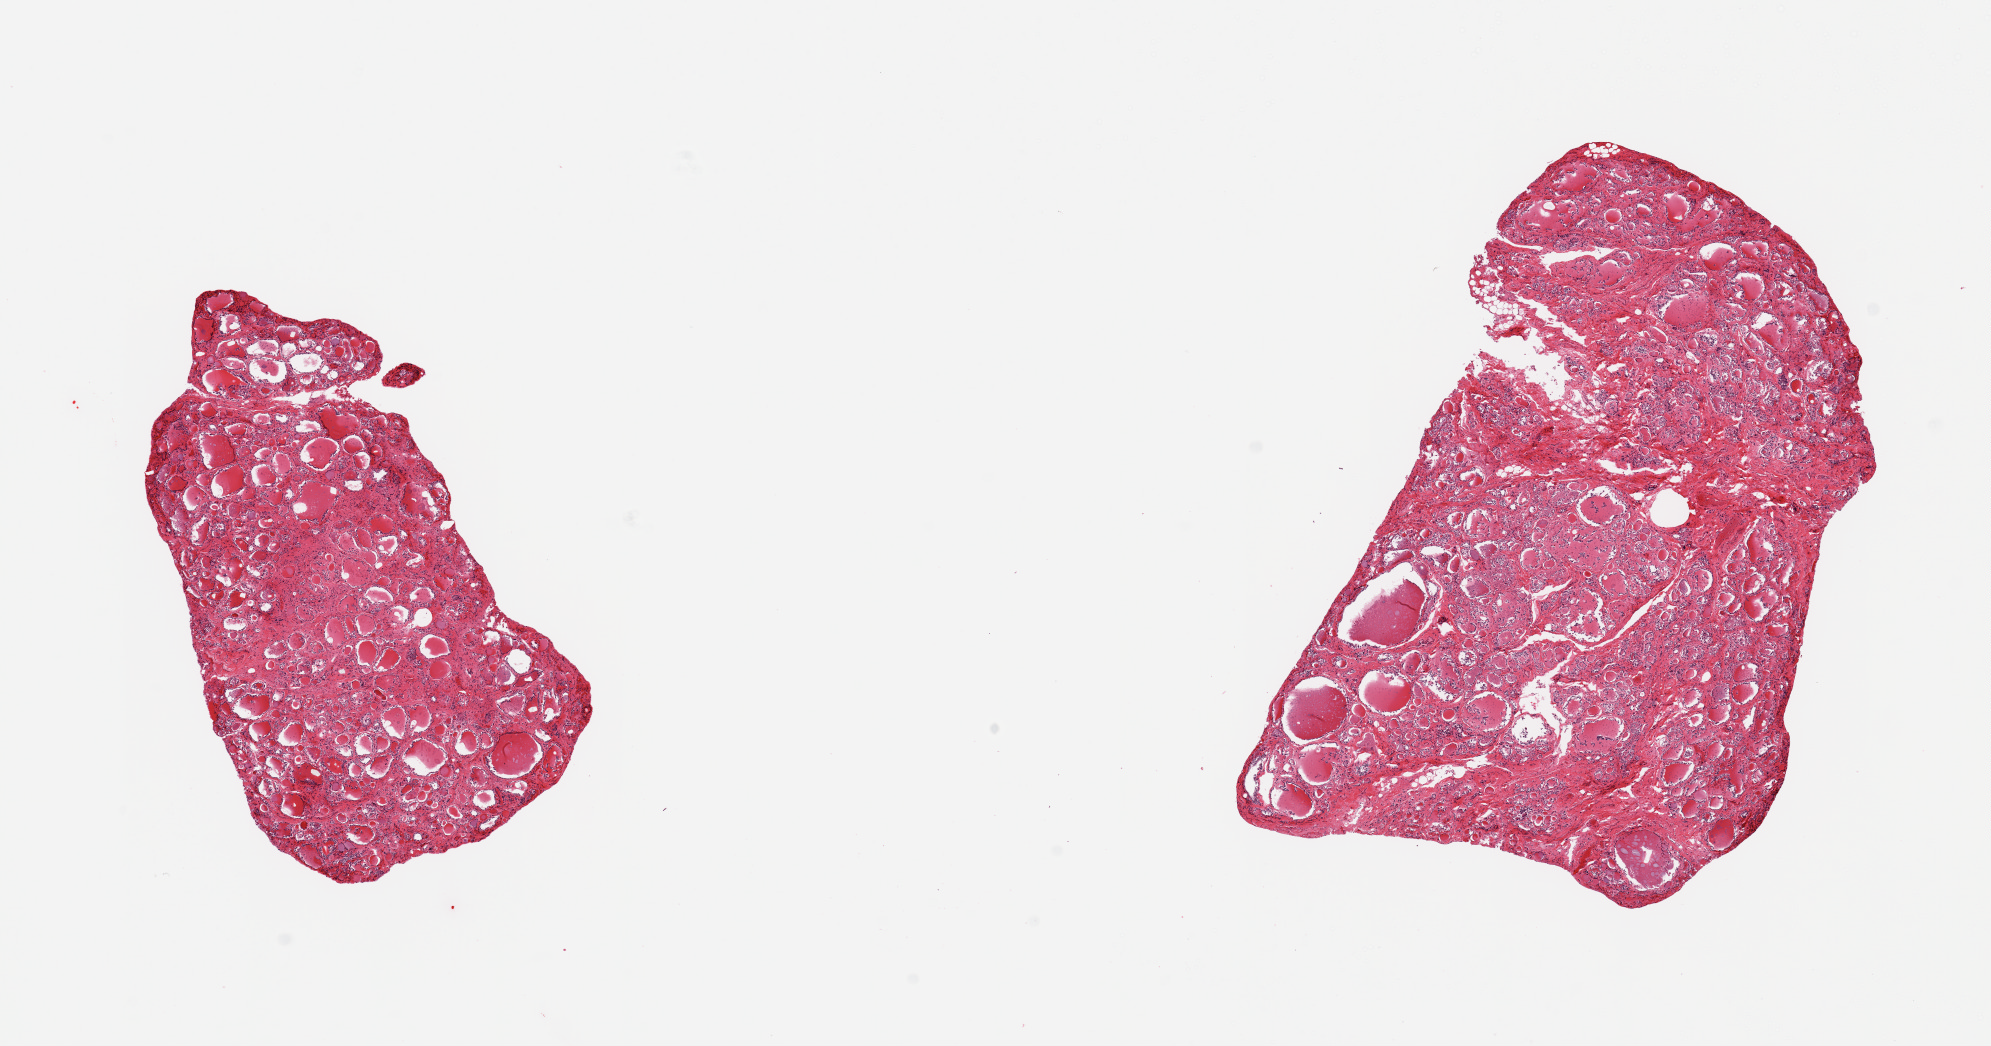
Digitized haematoxylin and eosin-stained section, brightfield, low-resolution overview of the scanned area, about 15.8 x 8.3 mm. PAXgene-fixed, paraffin-embedded tissue. Sampled site (target tissue): thyroid. Donor tissue sample. Male donor.
Reviewer comment on this tissue sample: 2 pieces; some interstitial fibrosis.